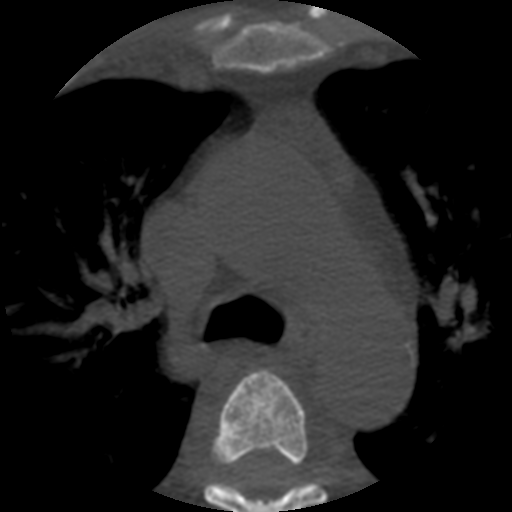
CT including the spine, one axial slice; slice 393 of 508 in the series (ordered by position); reconstruction kernel STANDARD; 120 kVp; bone window (W 1800 / L 400 HU); 1.25 mm slice thickness; 512 × 512 image matrix. Patient age 57 years. From the clinical record (not read from this slice): primary cancer: prostate.
Outlined on this slice (semi-automatic segmentation, software-assisted and operator-edited):
- T3 vertebra: bounding box <254,371,273,376> (left, top, right, bottom; pixels)
- T4 vertebra: <204,373,328,512>
- T5 vertebra: <214,481,317,494>